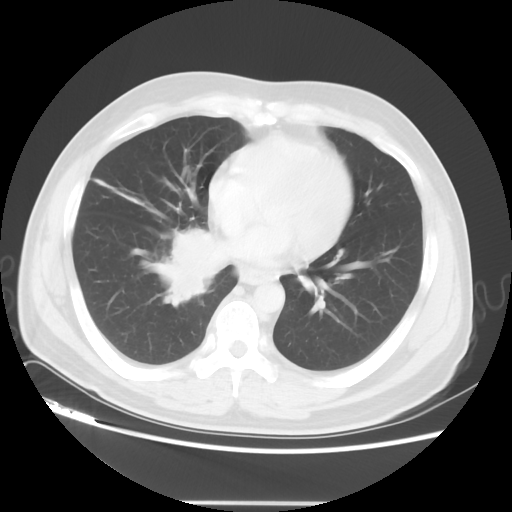
Chest CT, one axial slice; slice 19 of 48 in the series (ordered by position); 120 kVp; lung window (W 1500 / L -600 HU); 5 mm slice thickness; 512 × 512 image matrix, field of view 390 × 390 mm. Male patient, age 53 years. Case-level facts recorded for this patient, not image findings: clinical TNM (as recorded): T2 N3 M0; histopathological grade: G3.
Outlined on this slice (bounding box drawn by a radiologist):
- lung tumour (recorded histology: small cell carcinoma): bounding box <152,224,213,307> (left, top, right, bottom; pixels)